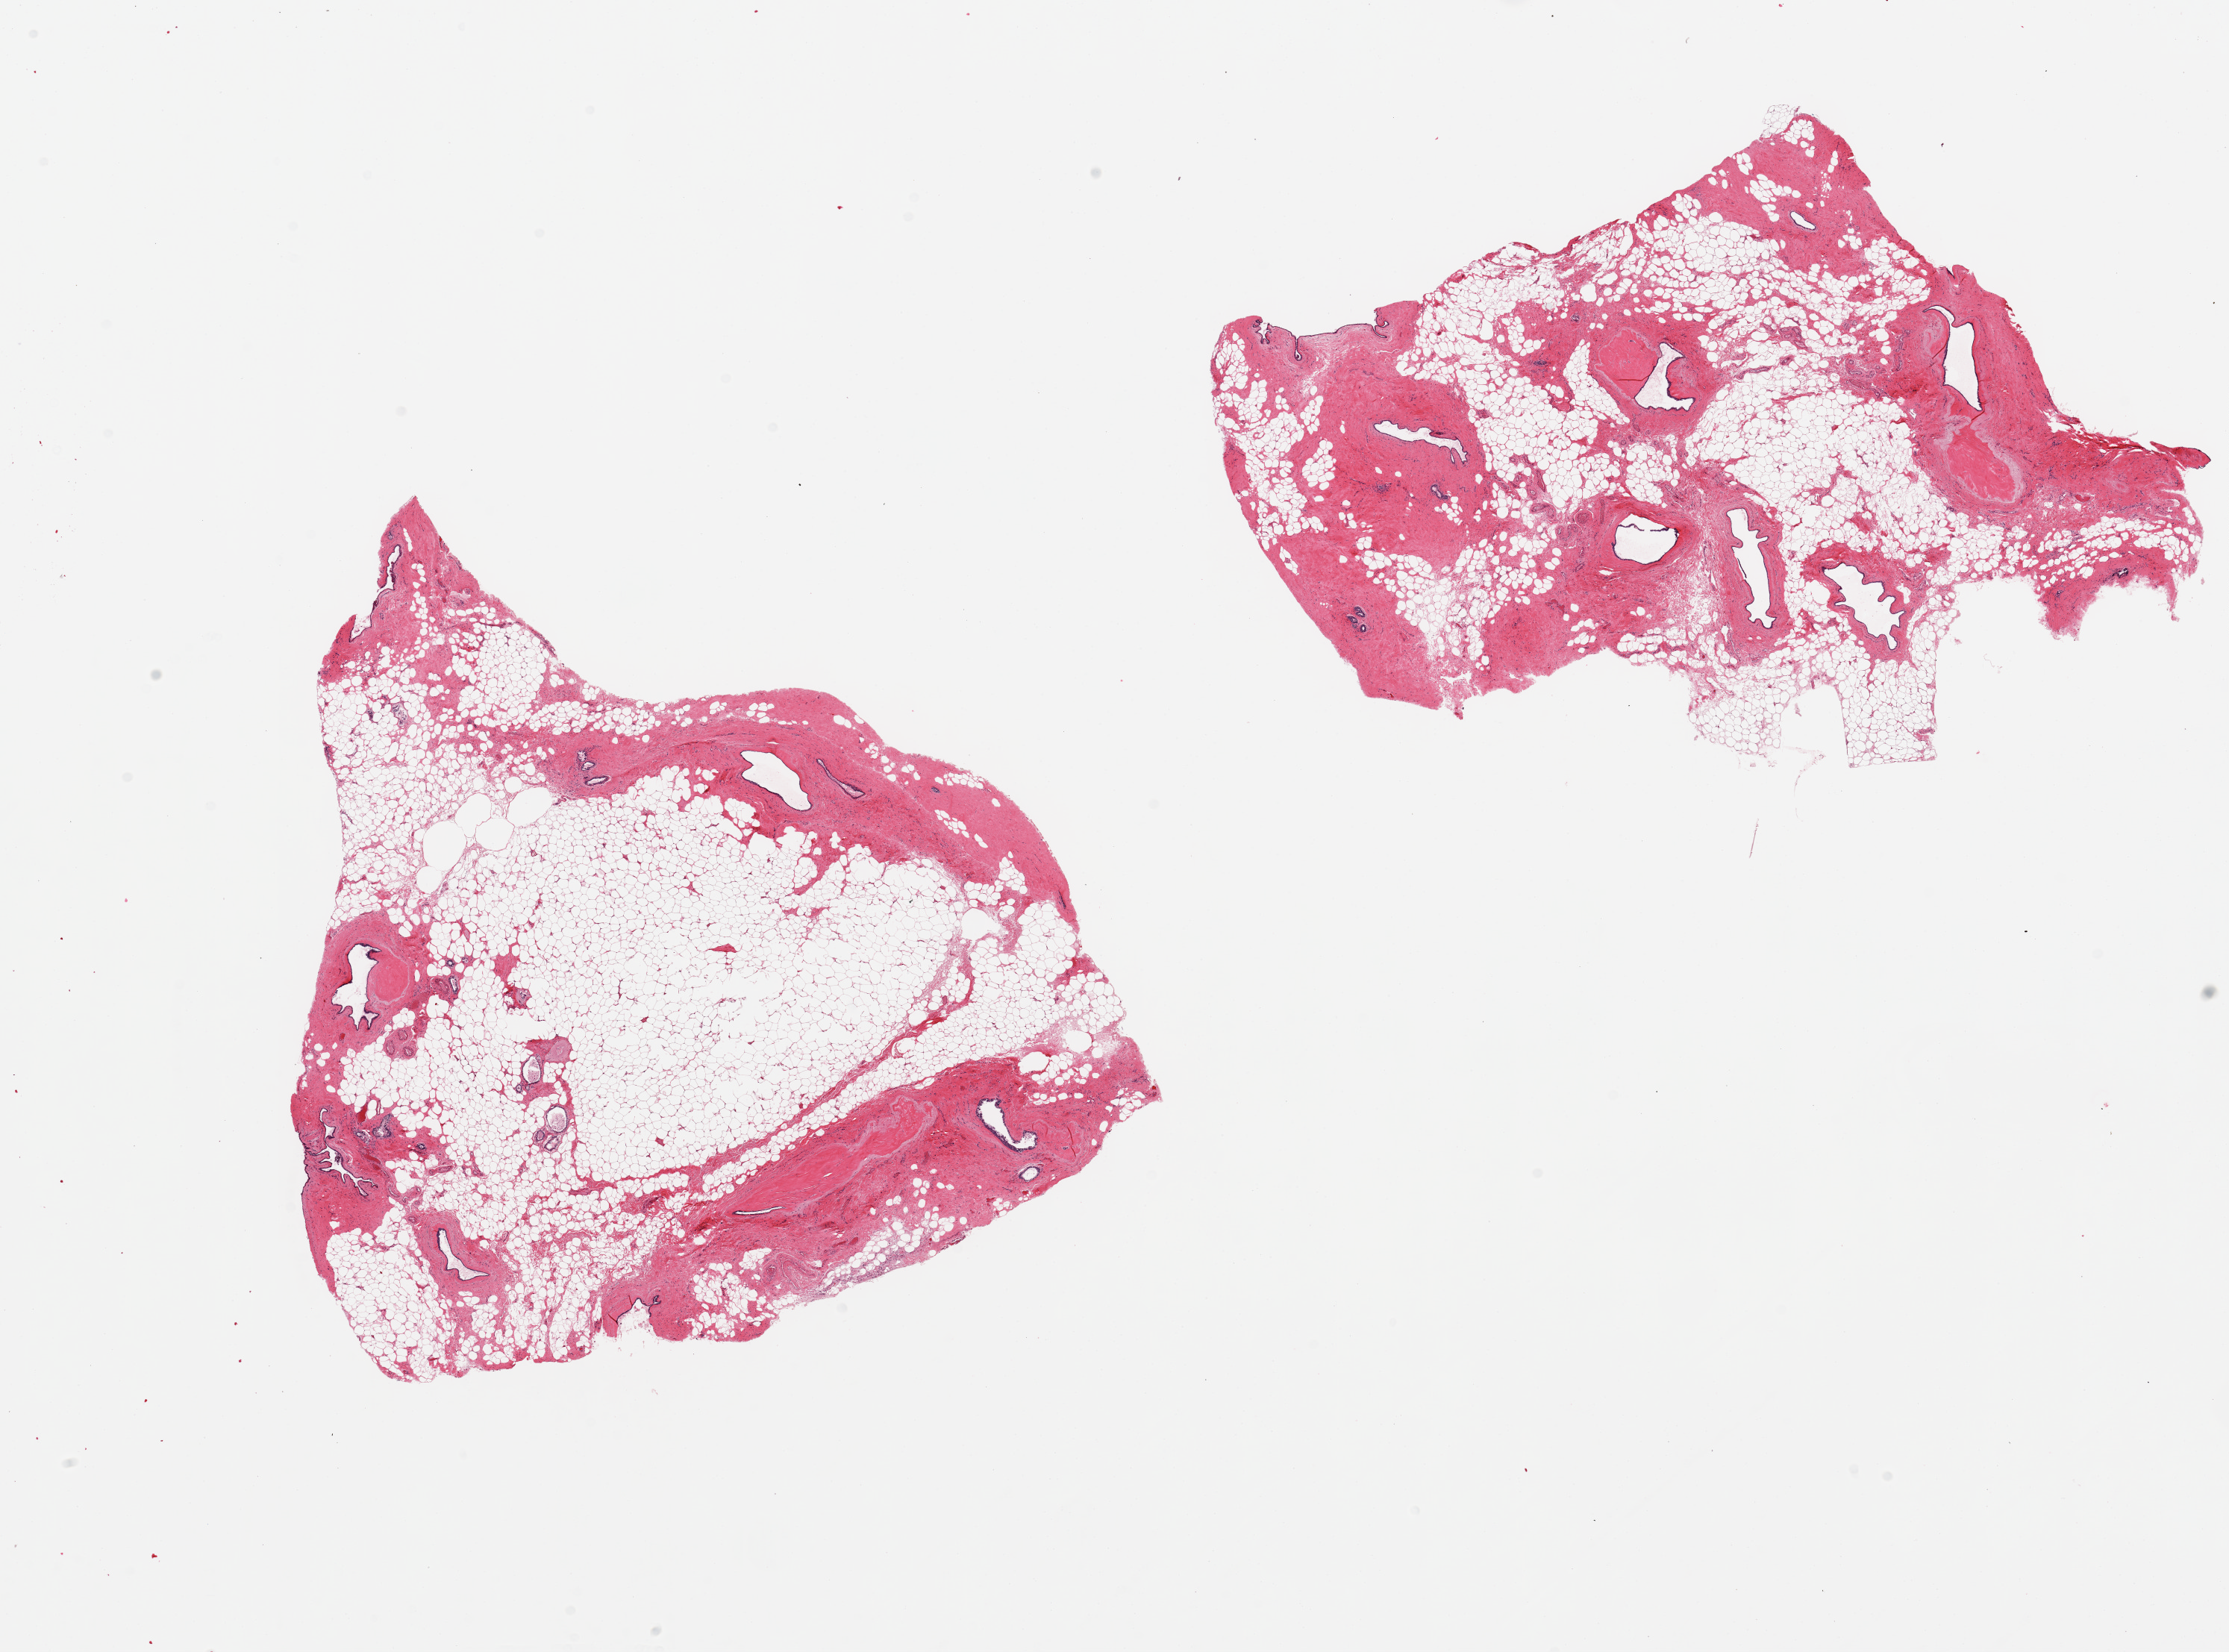
Haematoxylin and eosin whole-slide image, shown as a low-resolution overview of the whole scanned area (about 23.6 x 17.5 mm); PAXgene-fixed, paraffin-embedded tissue; sampled site (target tissue): breast; donor tissue sample. Female donor.
* pathologist's review note for this sample: 2 pieces; mammary duct ectasia